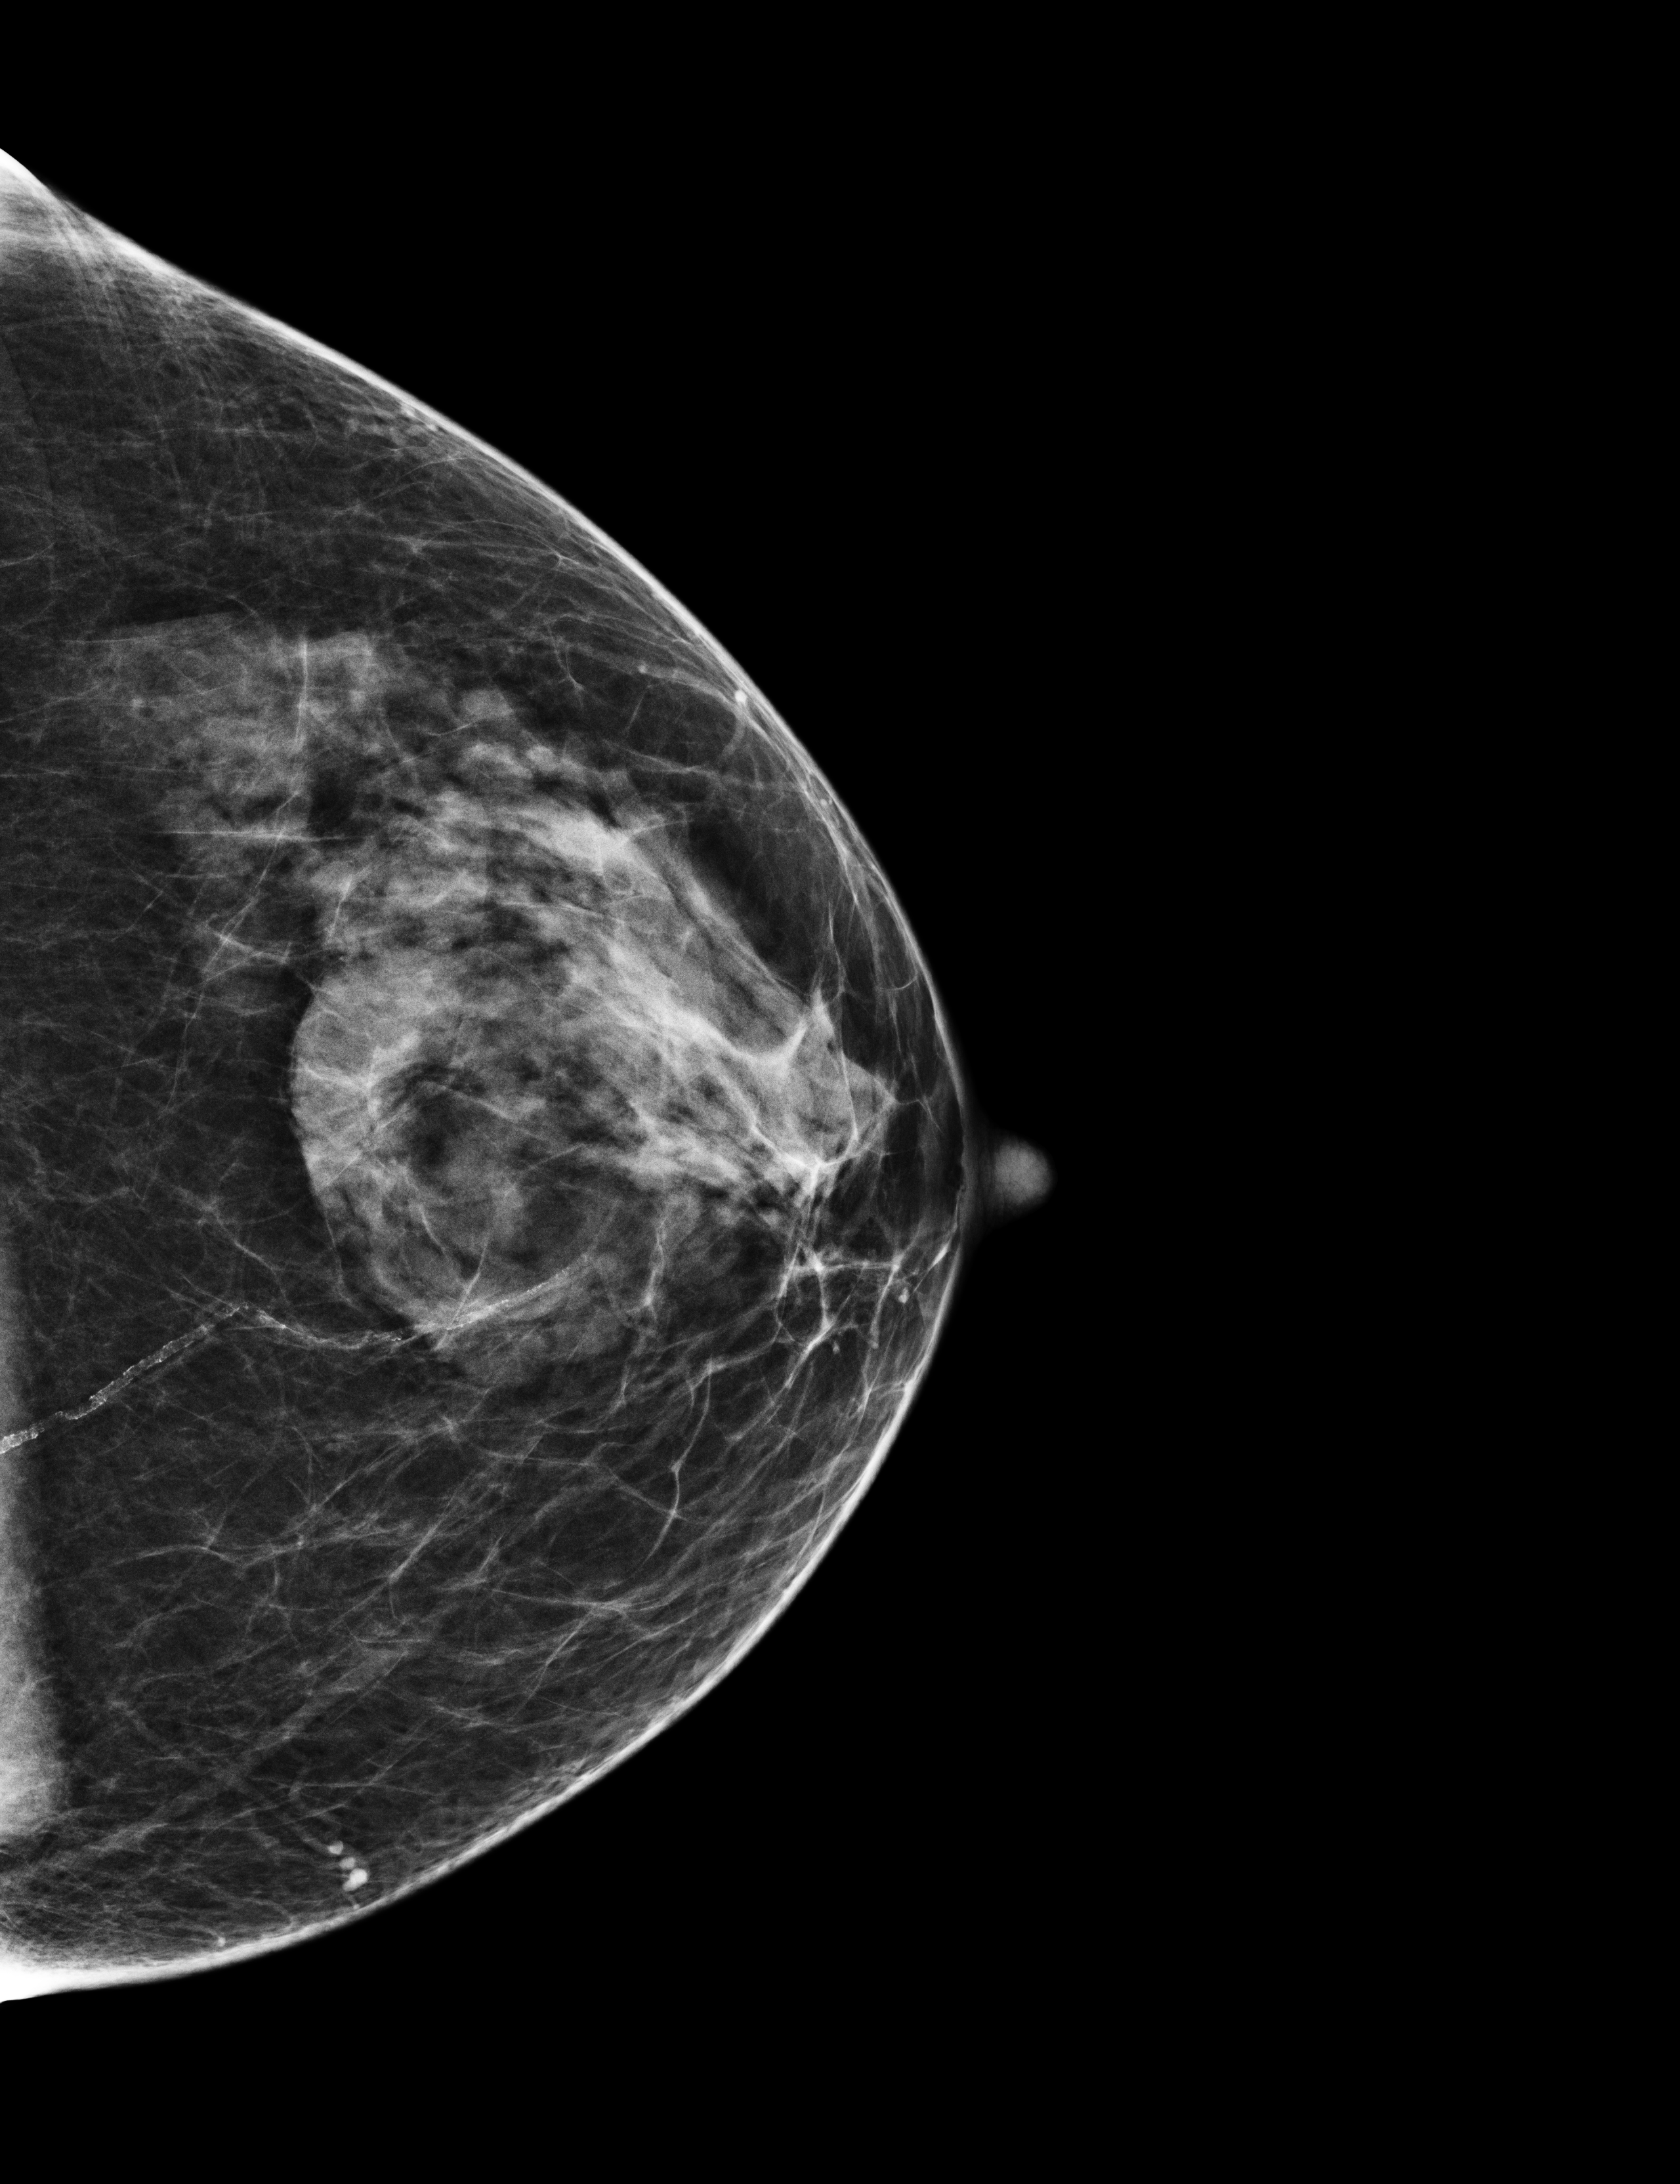
Screening examination, compressed breast thickness 43 mm, system: Selenia Dimensions. Female patient, age 58 years.
Image type: full-field digital mammogram. Breast: left. Projection: cranio-caudal projection.